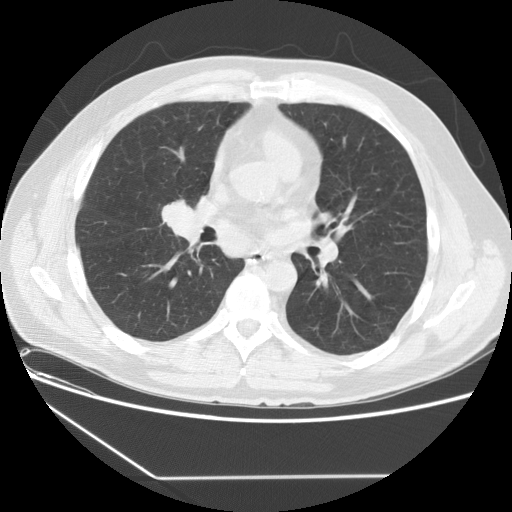
Low-dose screening chest CT, one axial slice; slice 79 of 154 in the series (ordered by position); lung window (W 1500 / L -600 HU); 512 × 512 image matrix.
Outlined on this slice (manually delineated by an expert):
- lesion 1 (tumor, middle lobe of right lung): bounding box <164,202,202,240> (left, top, right, bottom; pixels)